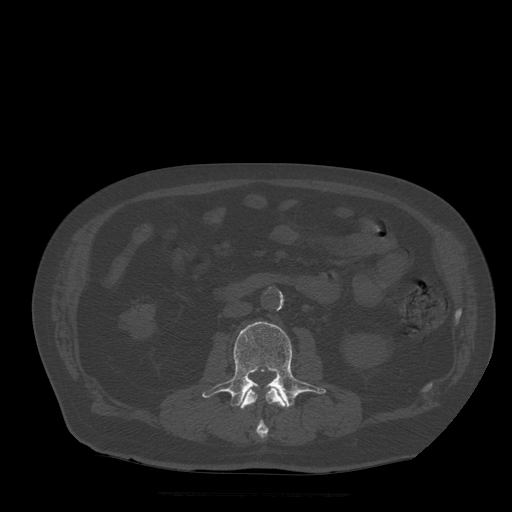
CT including the spine, one axial slice. Position 147 of 522 along the scan axis. Bone window (W 1800 / L 400 HU). 512 × 512 image matrix, field of view 420 × 420 mm. Patient age 72 years. From the clinical record (not read from this slice): primary cancer: prostate.
Structures marked on this image (semi-automatically segmented with operator editing):
- L2 vertebra: bounding box (x1, y1, x2, y2) in pixels: (240, 383, 288, 439)
- L3 vertebra: (202, 322, 326, 408)